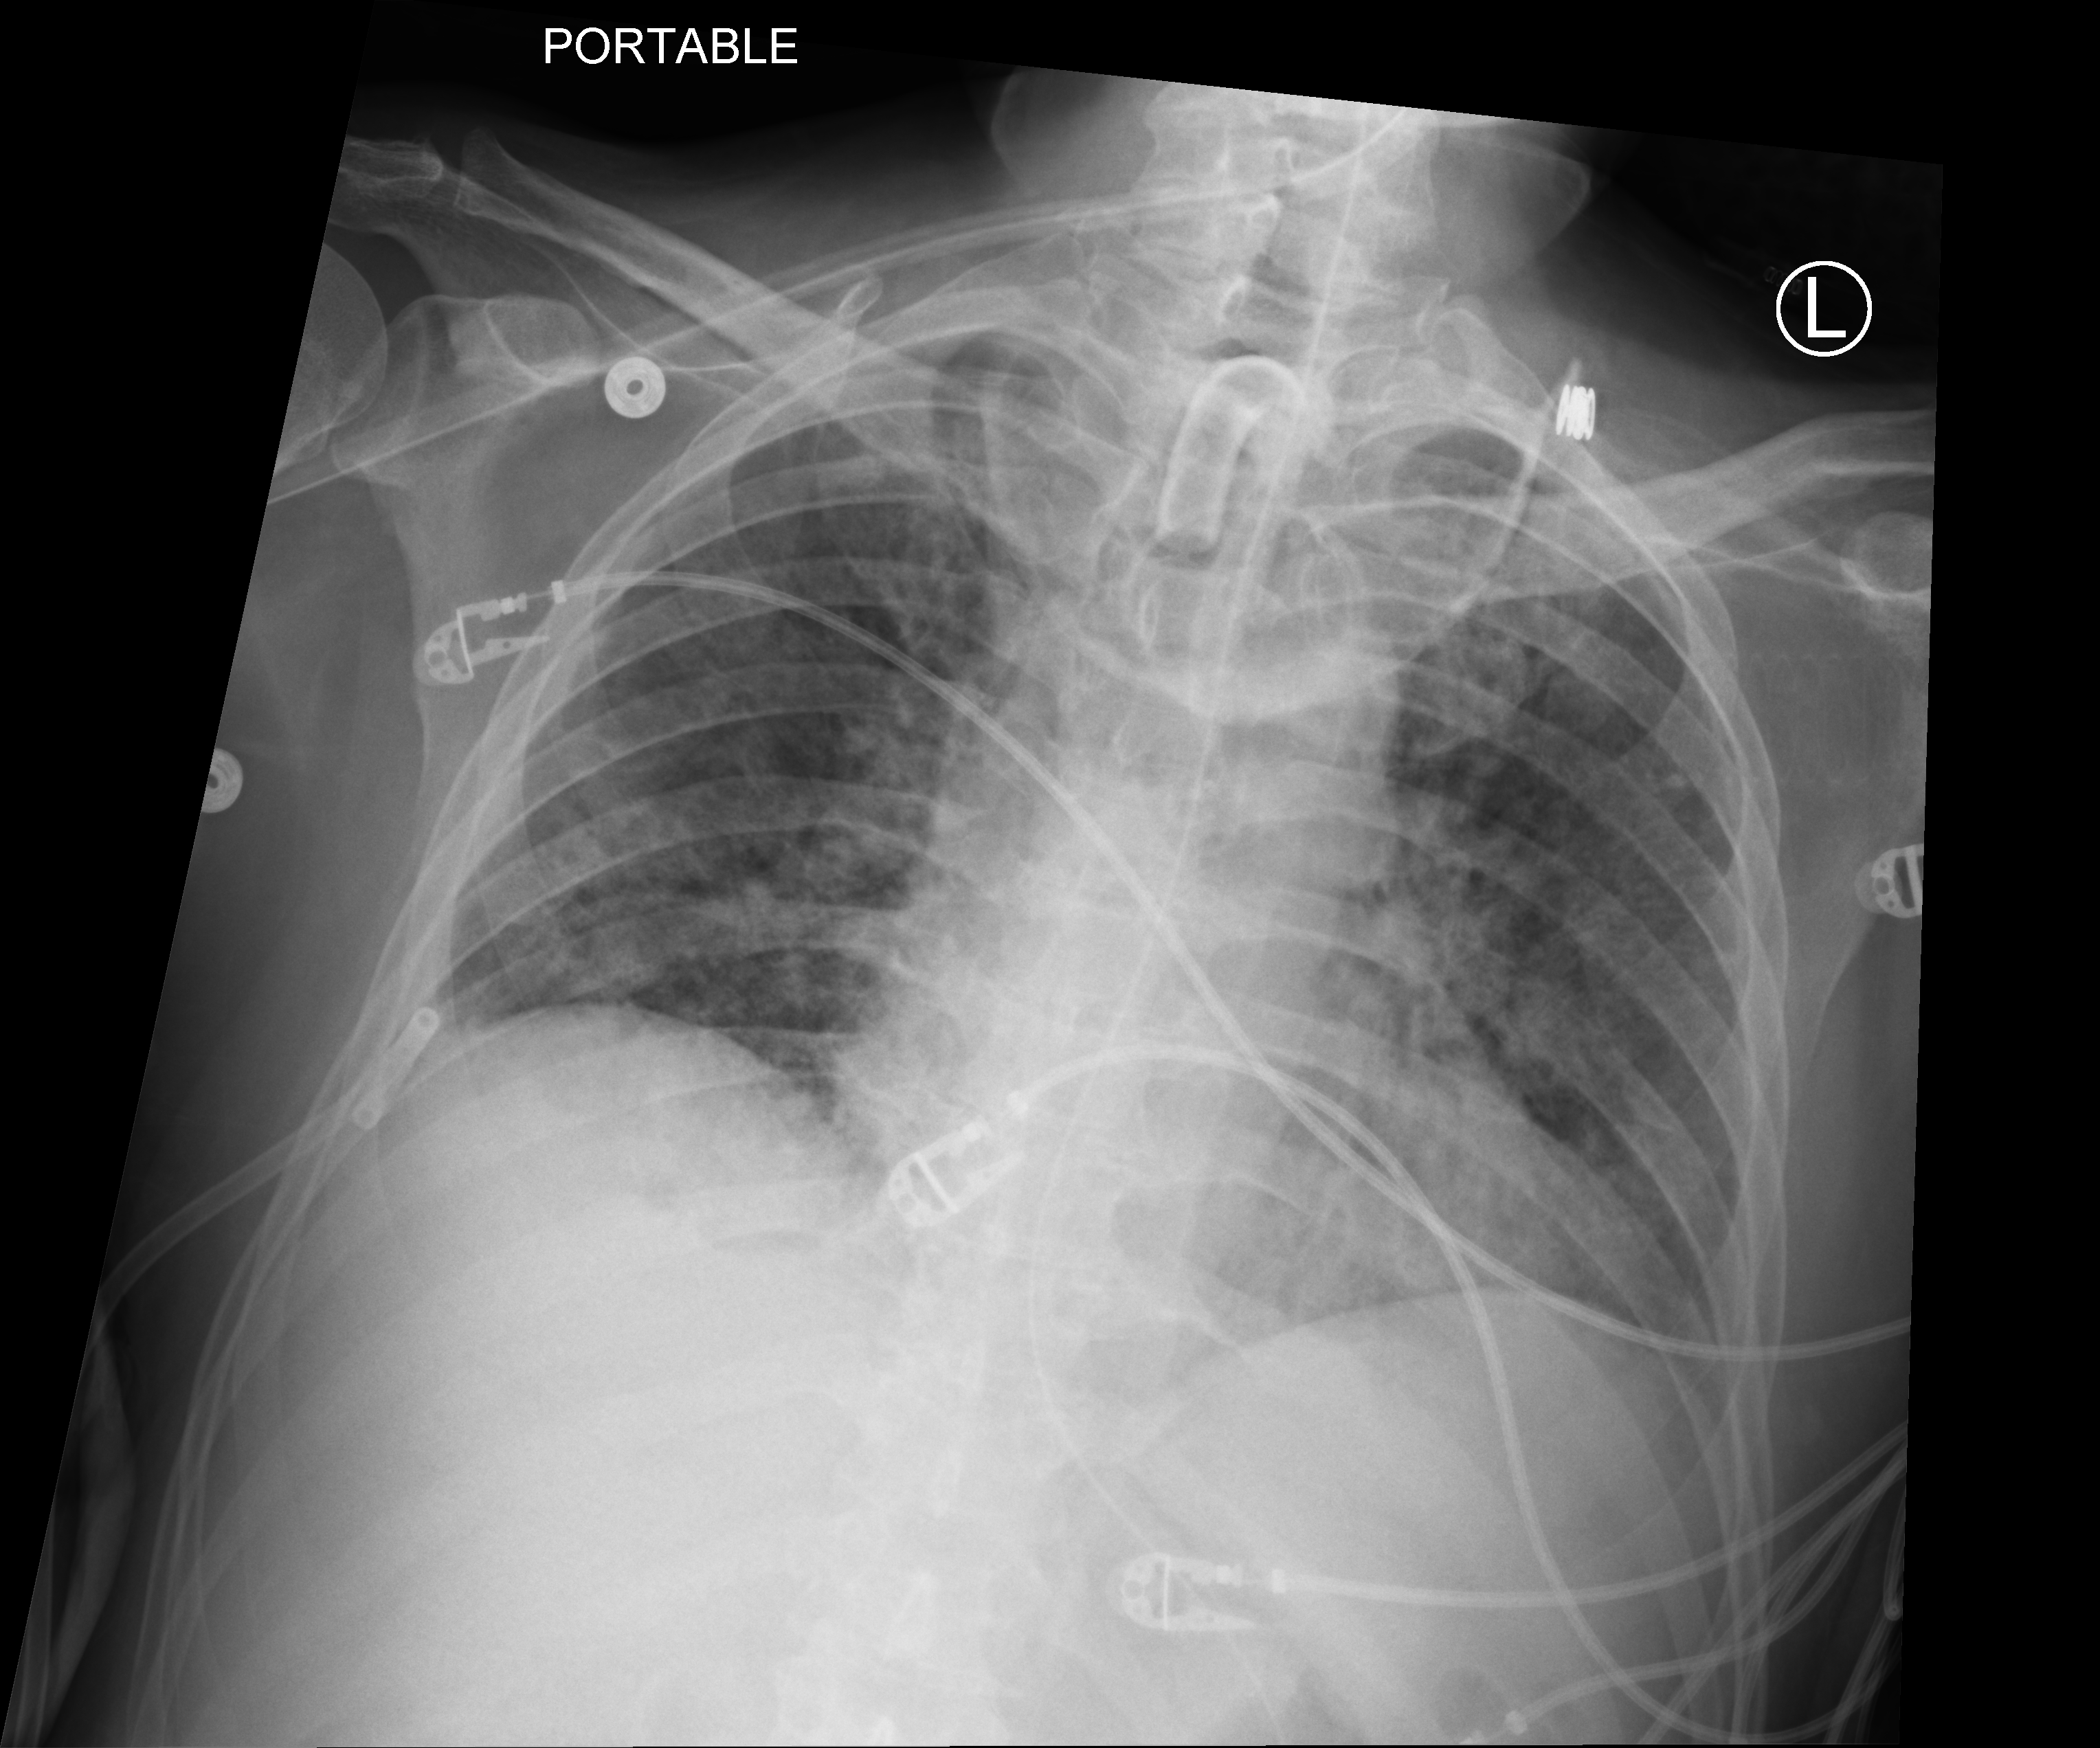
Chest X-ray (portable), anteroposterior (AP) projection. Male patient hospitalised with COVID-19, age 18–59 years.
From the hospital-stay record, not from the radiograph (when in the stay this image was taken is not recorded):
- COPD (admission record): no
- mechanically ventilated during this hospital stay: yes
- smoking status (admission record): never